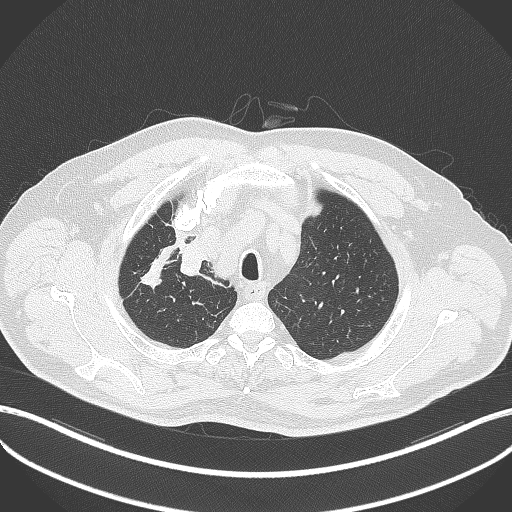
Chest CT, one axial slice. Position 323 of 411 along the scan axis. 120 kVp. Lung window (W 1500 / L -600 HU). 1 mm slice thickness. 512 × 512 image matrix, field of view 400 × 400 mm. Male patient, age 60 years. From the clinical record (not read from this slice): clinical TNM (as recorded): T1b N1 M0.
Annotated regions visible in this slice (bounding box drawn by a radiologist):
- lung tumour (recorded histology: squamous cell carcinoma): box from (x=175, y=235) to (x=212, y=278) px